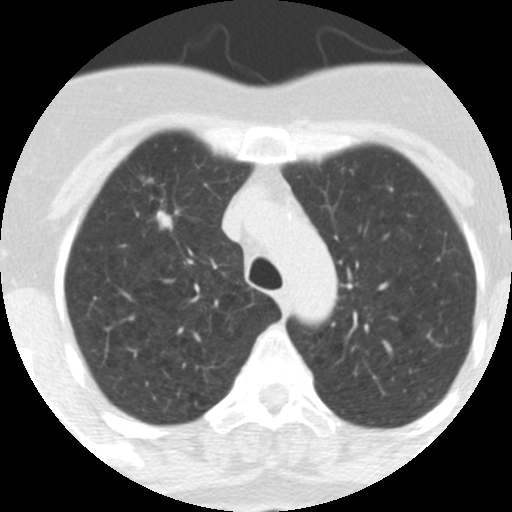
Axial slice from a low-dose chest CT screening exam, baseline annual screen, lung window (W 1500 / L -600 HU), 2.5 mm slice thickness, standard (soft-tissue) reconstruction kernel (STANDARD), 120 kVp, slice 71 of 313 in the series, 512 × 512 image matrix, field of view 253 × 253 mm. Female participant, aged 62 years at enrolment.
Expert-annotated lung lesion, bounding box [x1, y1, x2, y2] px = [116, 163, 184, 234]. The exam's reader record, not a measurement of the box and not confirmed to be the same lesion: non-calcified nodule or mass ≥4 mm, right upper lobe, 9 × 7 mm, spiculated (stellate) margins, soft tissue attenuation. Official screen result: positive, change unspecified: nodule(s) >= 4 mm or enlarging nodule(s), mass(es), or other non-specific abnormalities suspicious for lung cancer. Participant outcome: lung cancer diagnosed 126 days after this screen — adenocarcinoma, NOS, right upper lobe, moderately differentiated (G2), stage IA (AJCC 6th edition), 18 mm at pathology.